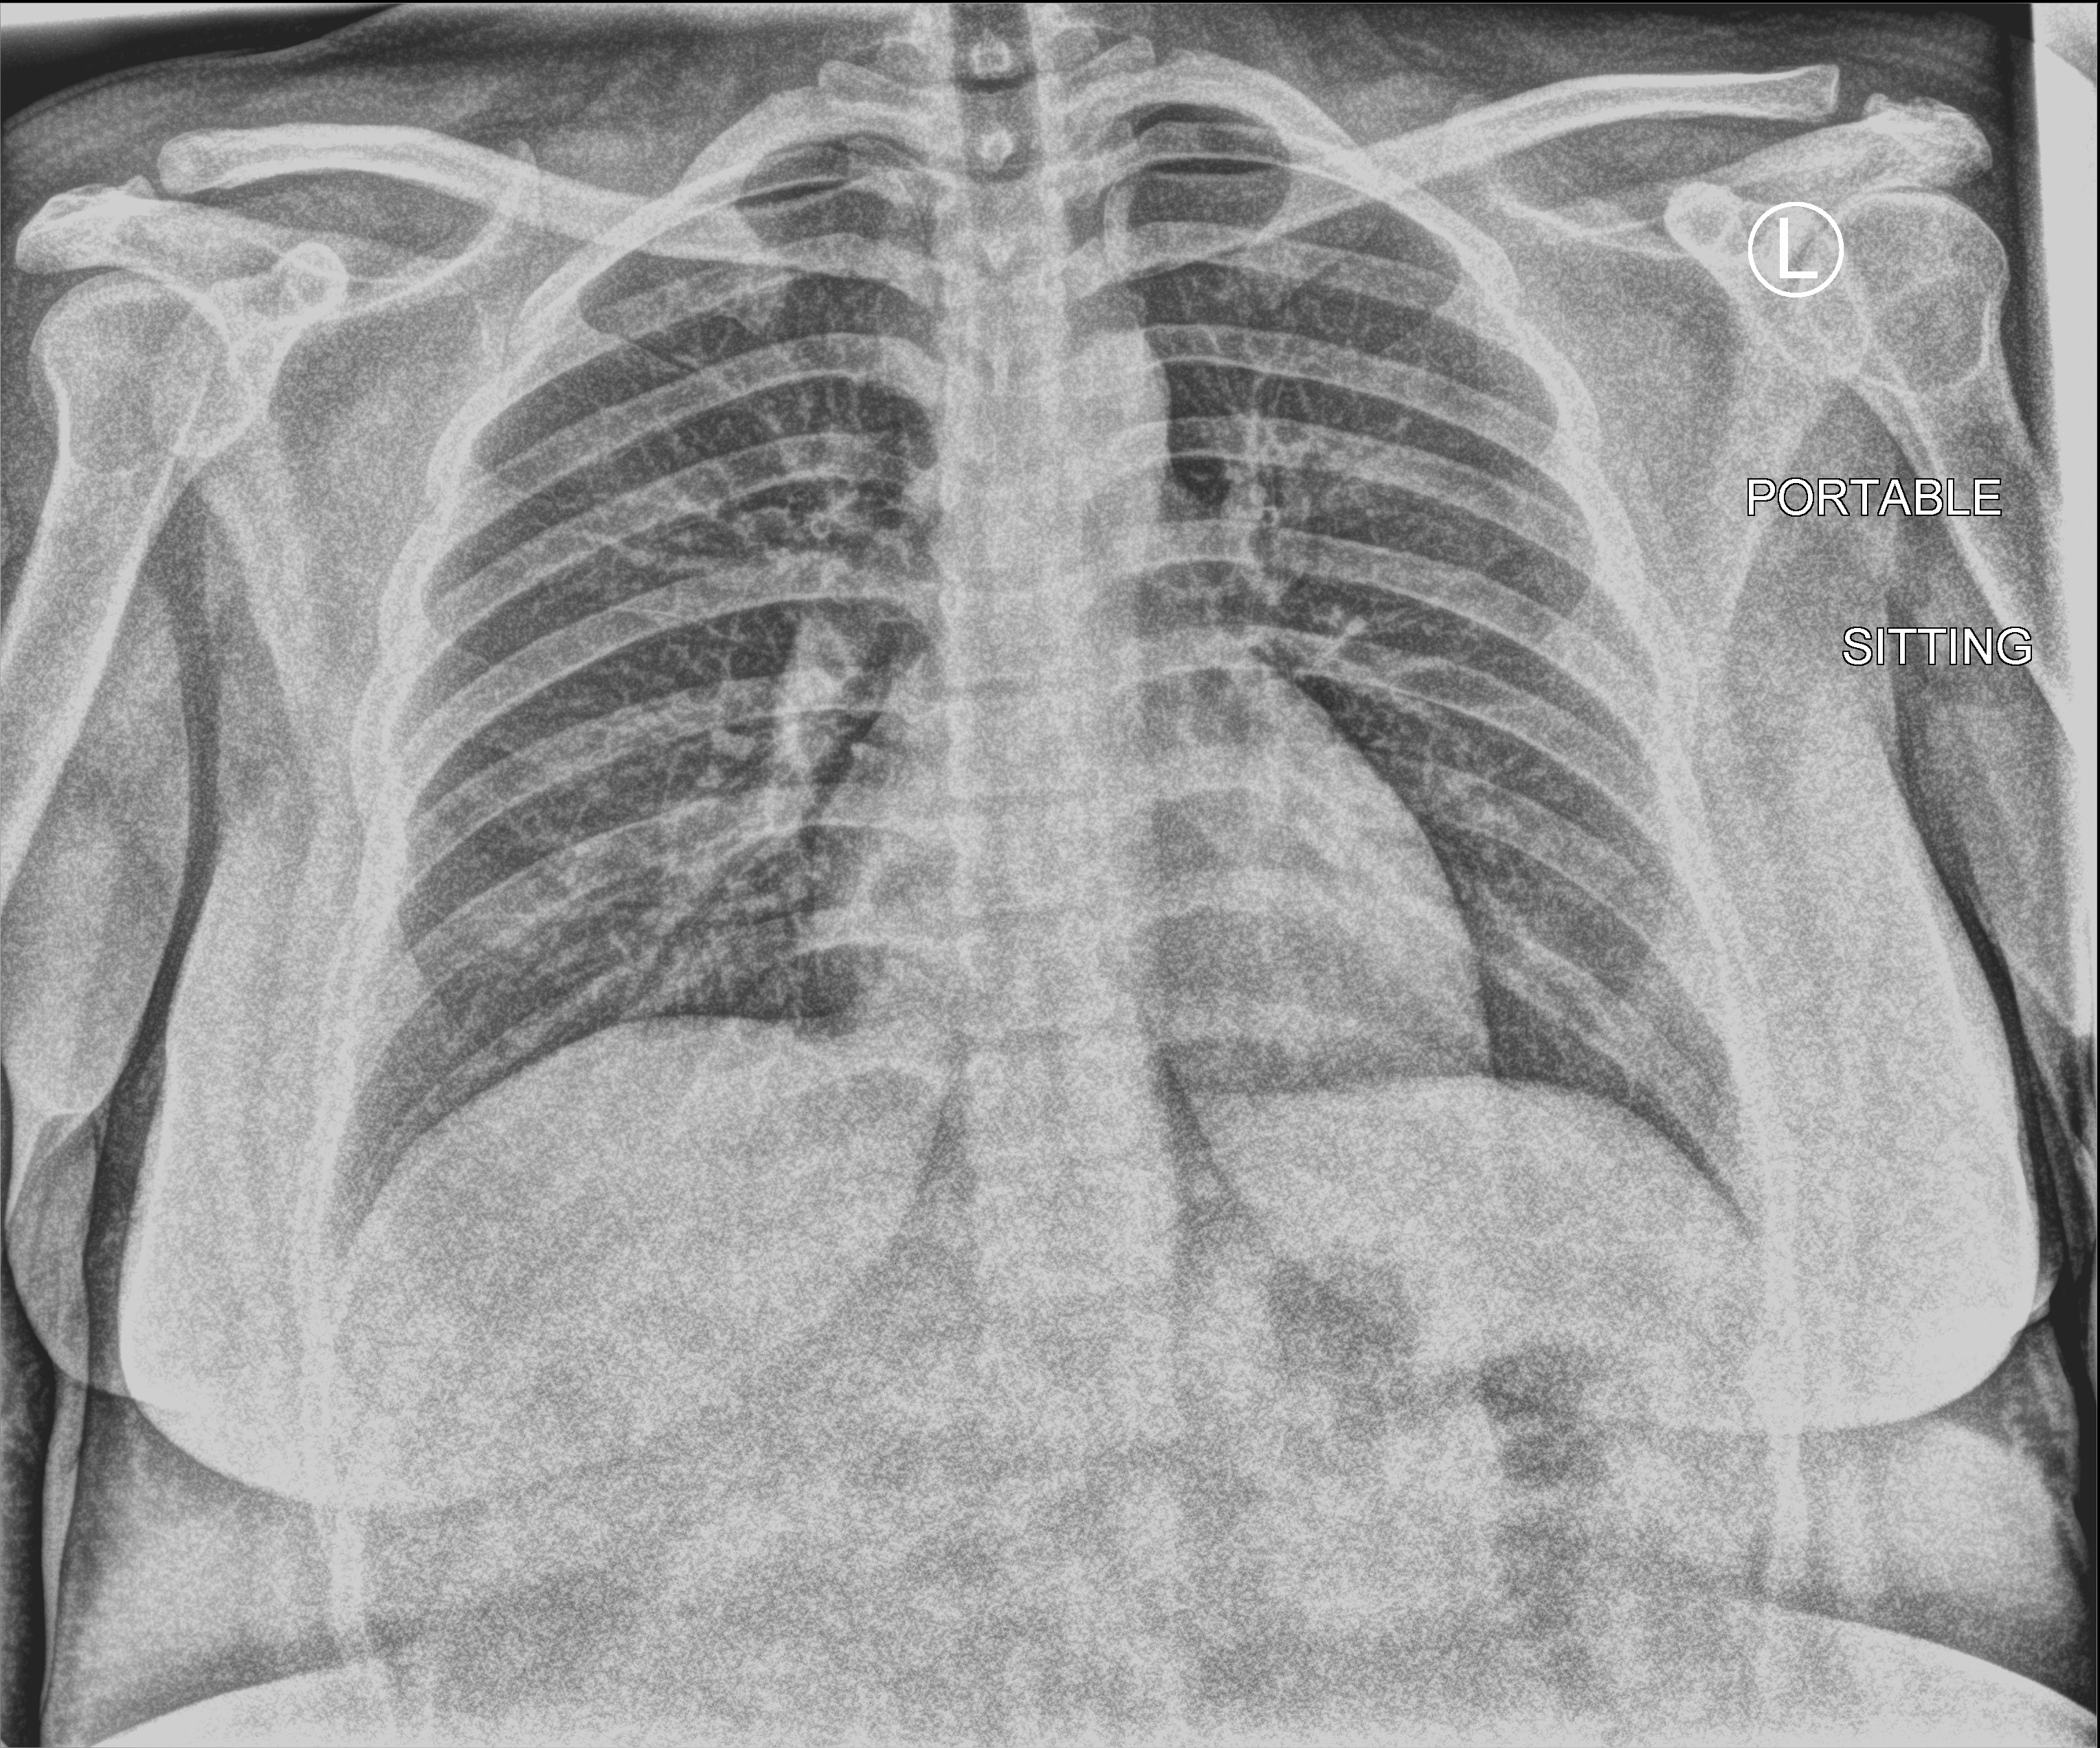
Portable chest radiograph; anteroposterior (AP) projection. Female patient hospitalised with COVID-19, age 18–59 years.
Hospital-stay facts (about this admission, not read from this image; timing relative to this image not recorded): mechanically ventilated during this hospital stay: no; diabetes (admission record): no.